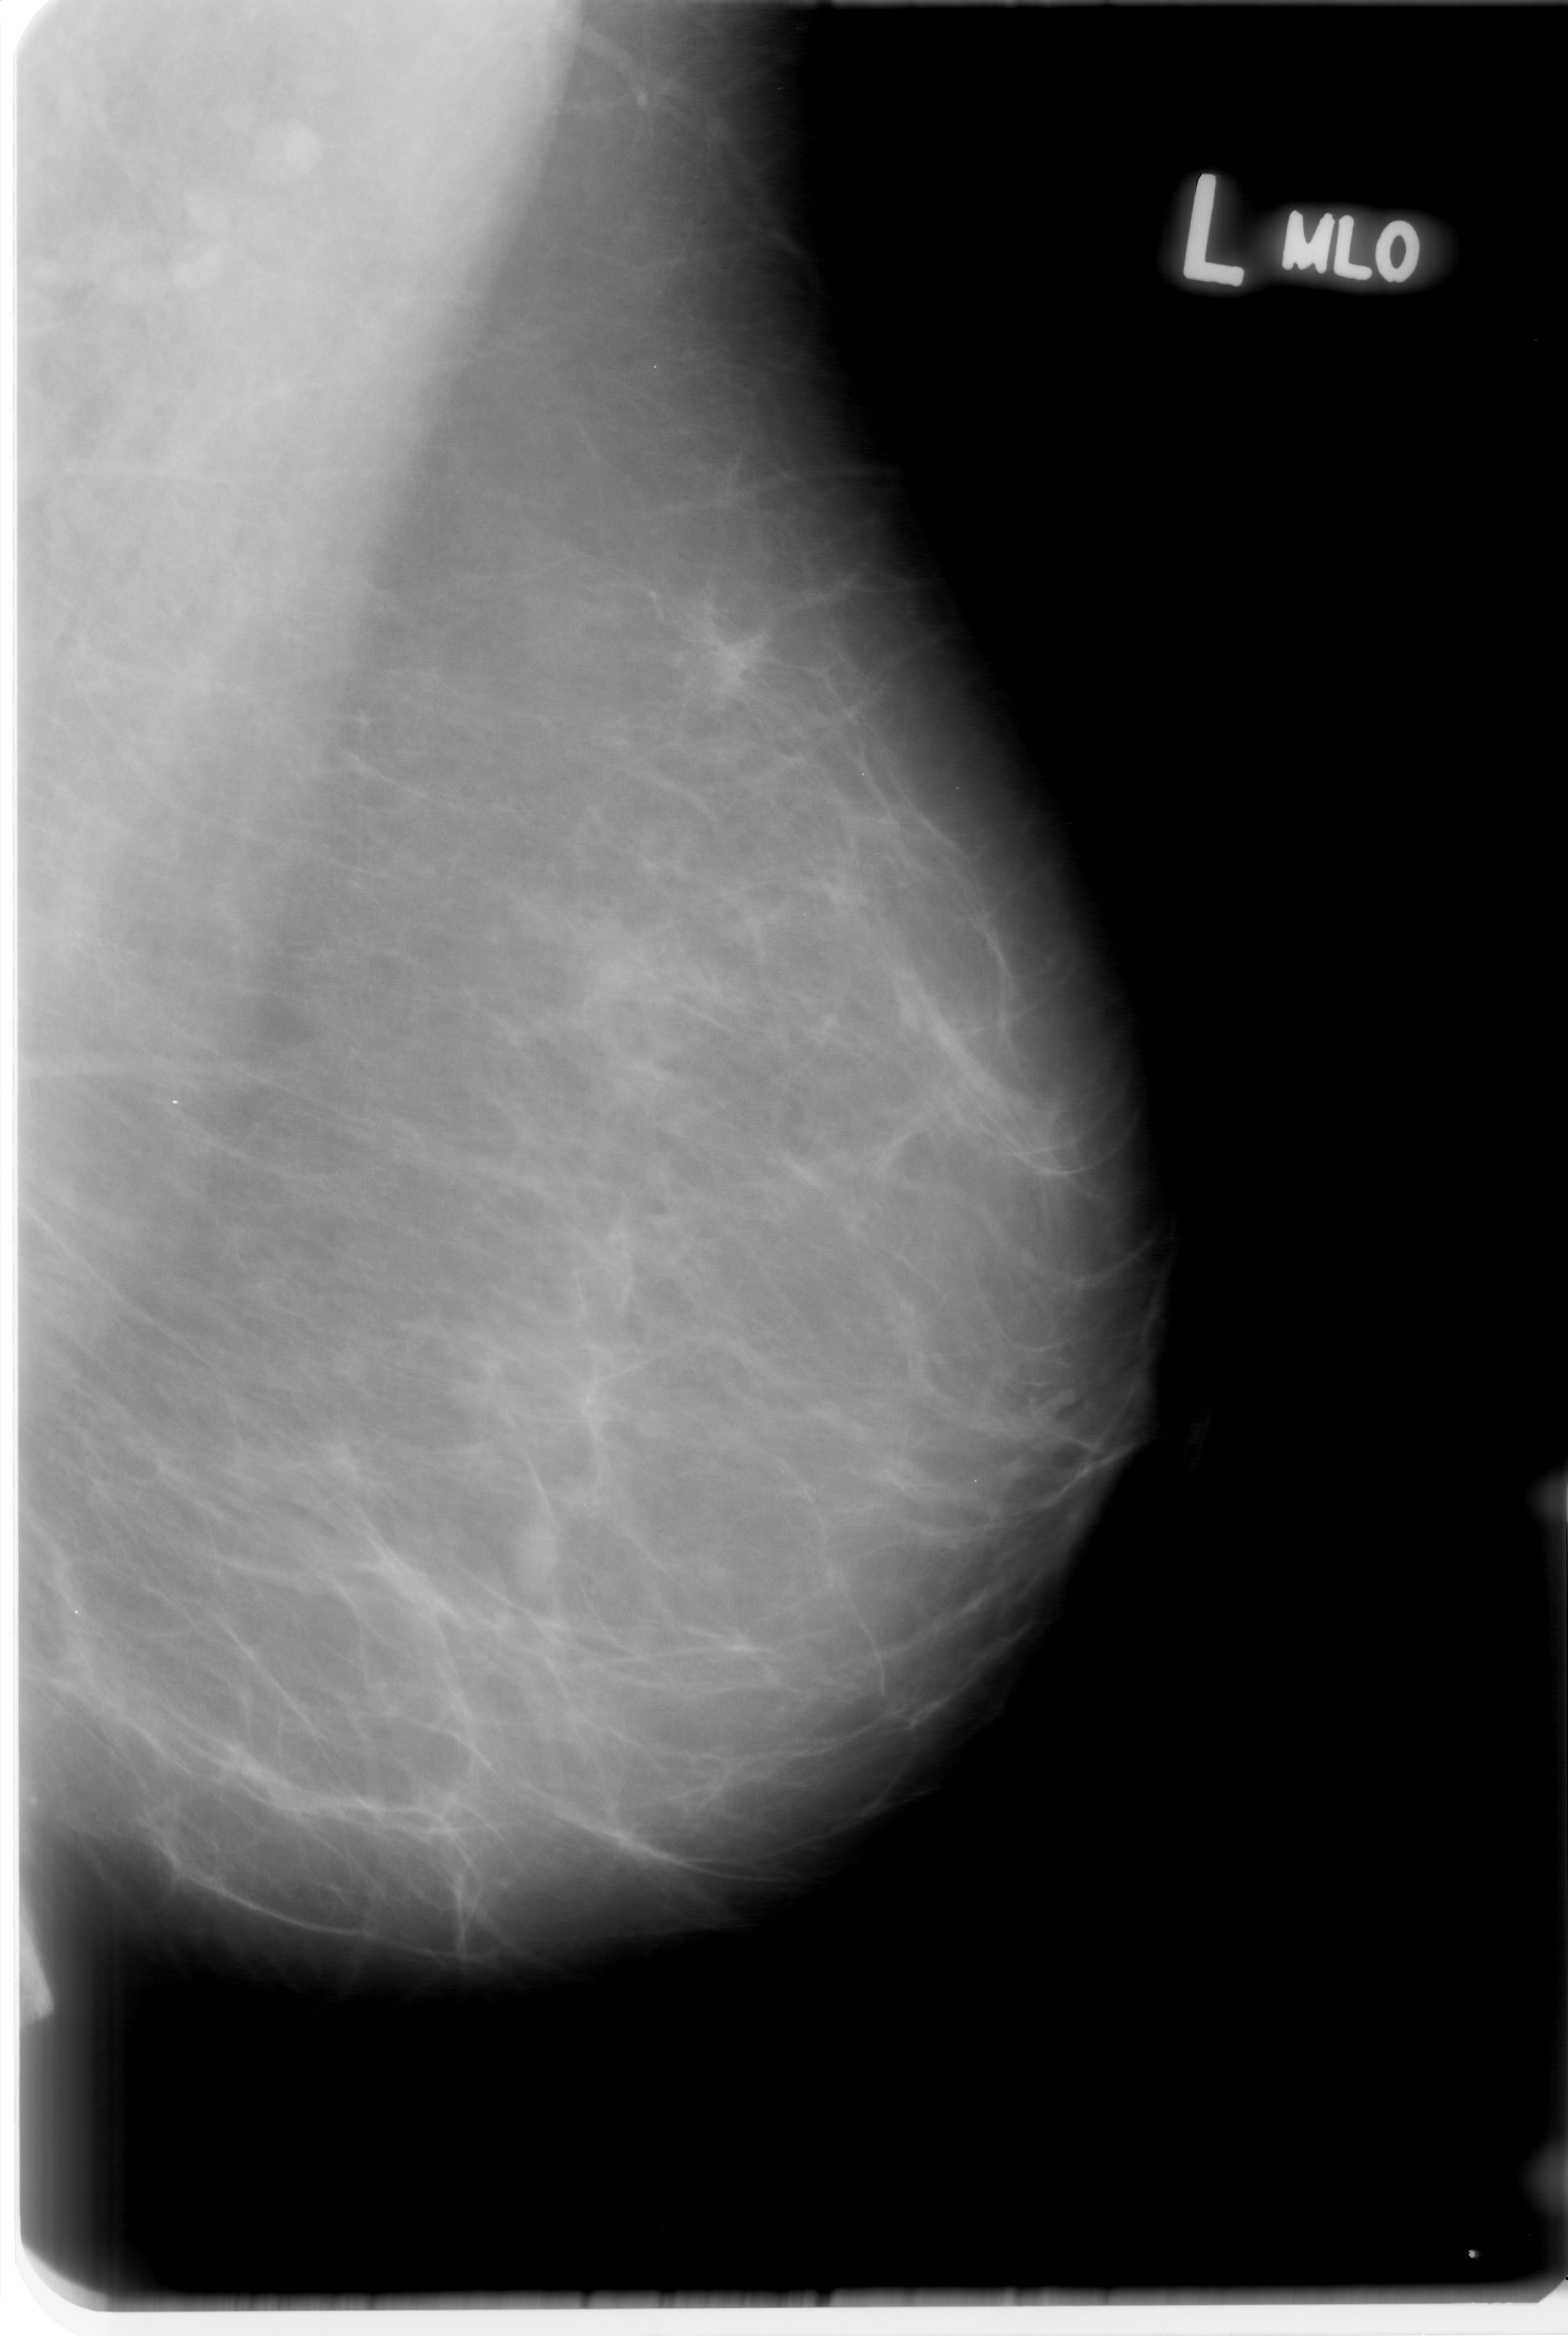
Digitized screen-film mammogram. Left breast. MLO view. 1568 × 2336 image matrix.
Marked abnormalities (boxes around the expert regions of interest):
- mass, shape oval, margins obscured; BI-RADS assessment category 0 (incomplete: needs additional imaging); subtlety rating 5 on a 1 (subtle) to 5 (obvious) scale; pathology (as recorded): benign: box from (x=374, y=1548) to (x=521, y=1662) px